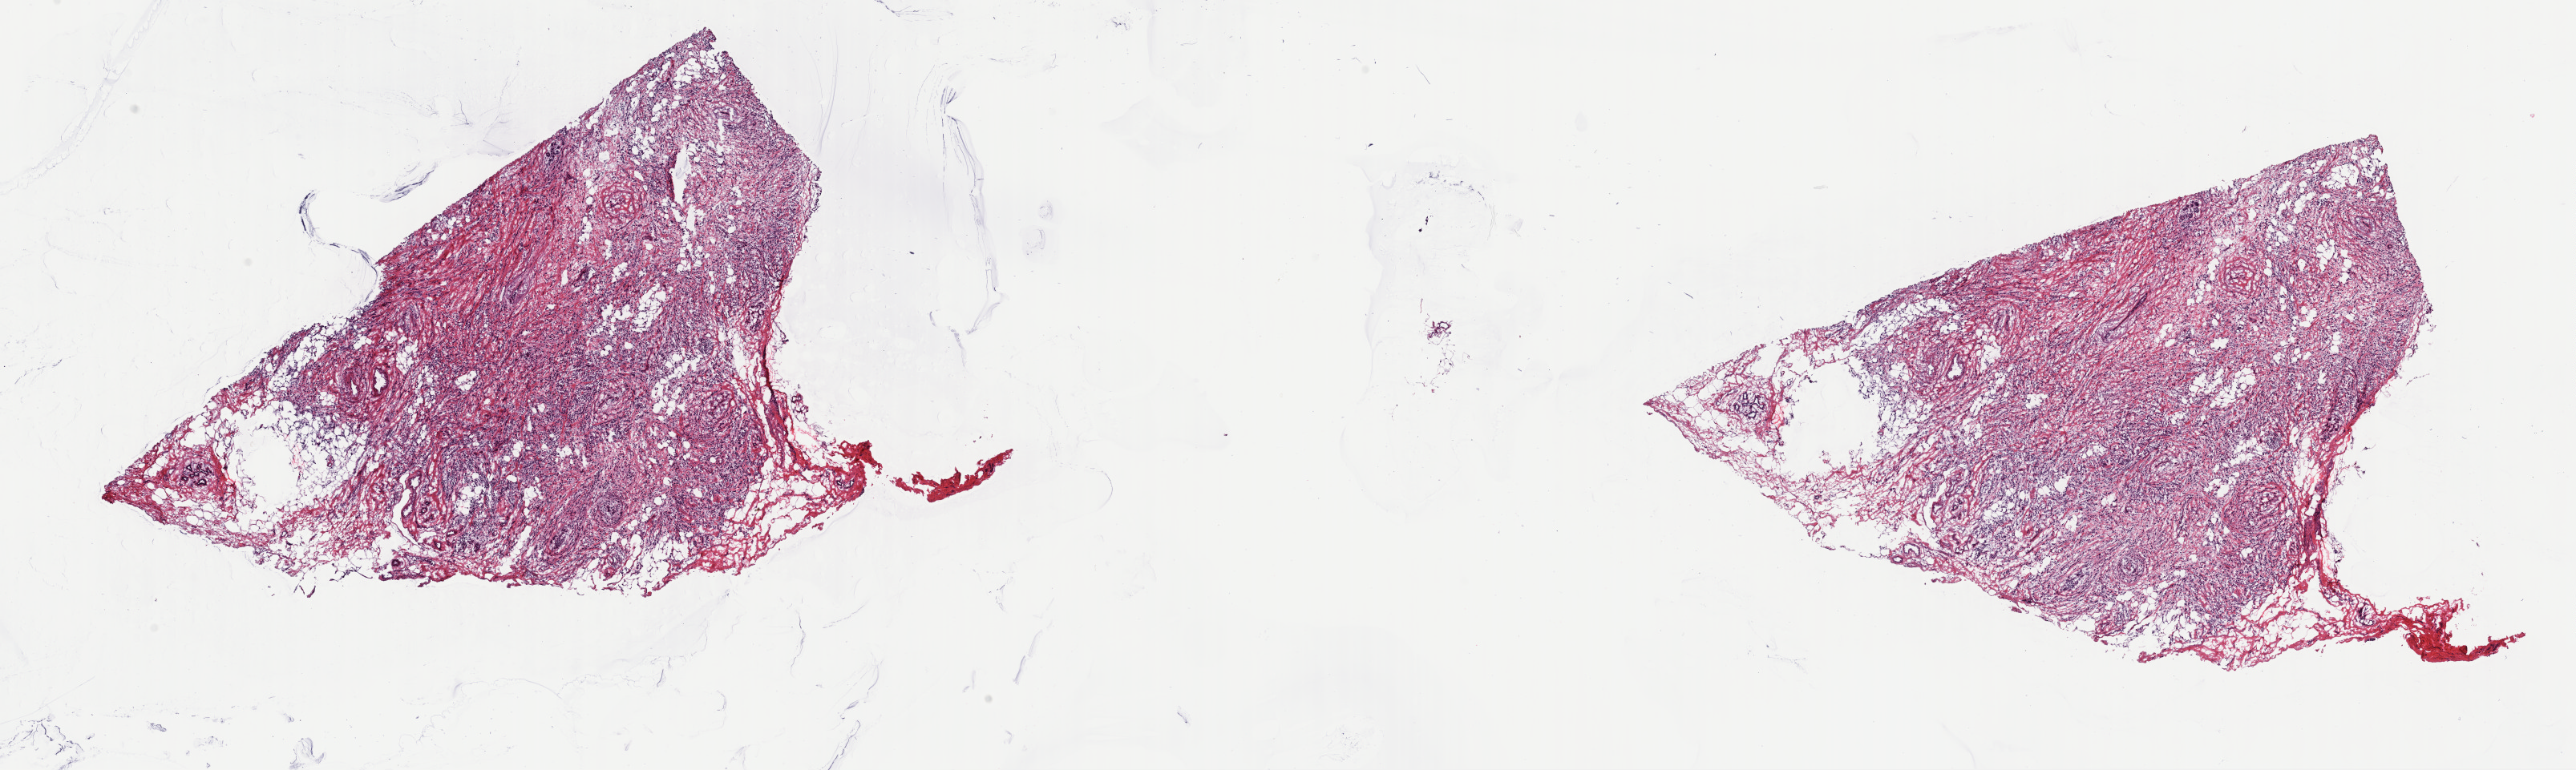
Whole-slide histology image, Hematoxylin and eosin (H&E) stained, whole scanned area (about 25.4 x 7.6 mm, from a 40x scan) shown as a low-resolution overview; frozen section from the top of the tissue portion; breast, primary tumour sample. Female patient; age at initial diagnosis 62 years. Slide review estimates, as recorded: tumour cells 70%, tumour nuclei 70%, normal cells 0%, stromal cells 20%, necrosis 10%. Infiltration values recorded for this section: lymphocyte infiltration 40%, monocyte infiltration 20%, neutrophil infiltration 20%.
• AJCC pathologic stage: IIA (6th edition)
• pathologic diagnosis: Lobular carcinoma, NOS